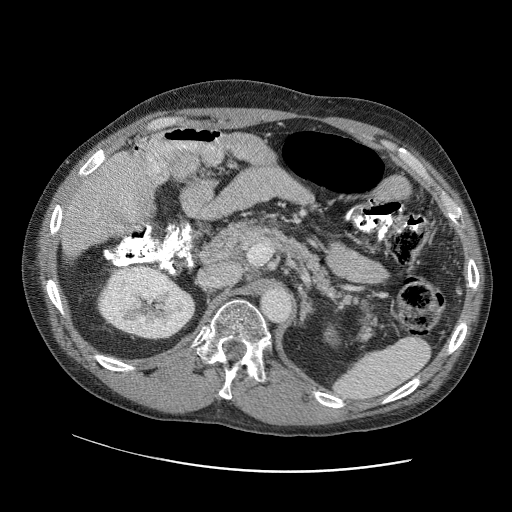
Contrast-enhanced abdominal CT (liver protocol), one axial slice; position 55 of 109 along the scan axis; reconstruction kernel STANDARD; 120 kVp; soft-tissue window (W 400 / L 40 HU); 2.5 mm slice thickness; 512 × 512 image matrix. From the clinical record (not read from this slice): diagnosis: hepatocellular carcinoma (patient treated with transarterial chemoembolisation; whether this scan precedes or follows treatment is not stated here); TNM stage (as recorded): Stage-IIIC; Child-Pugh class: B; tumour differentiation: well differentiated; tumour nodularity: uninodular.
Structures marked on this image (semi-automatic segmentation, software-assisted and operator-edited):
- liver parenchyma outside the tumour (the mass and vessels are separate outlines, so this box may not span the whole liver): bounding box (x1, y1, x2, y2) in pixels: (61, 146, 168, 256)
- liver vessels: (134, 150, 166, 184)